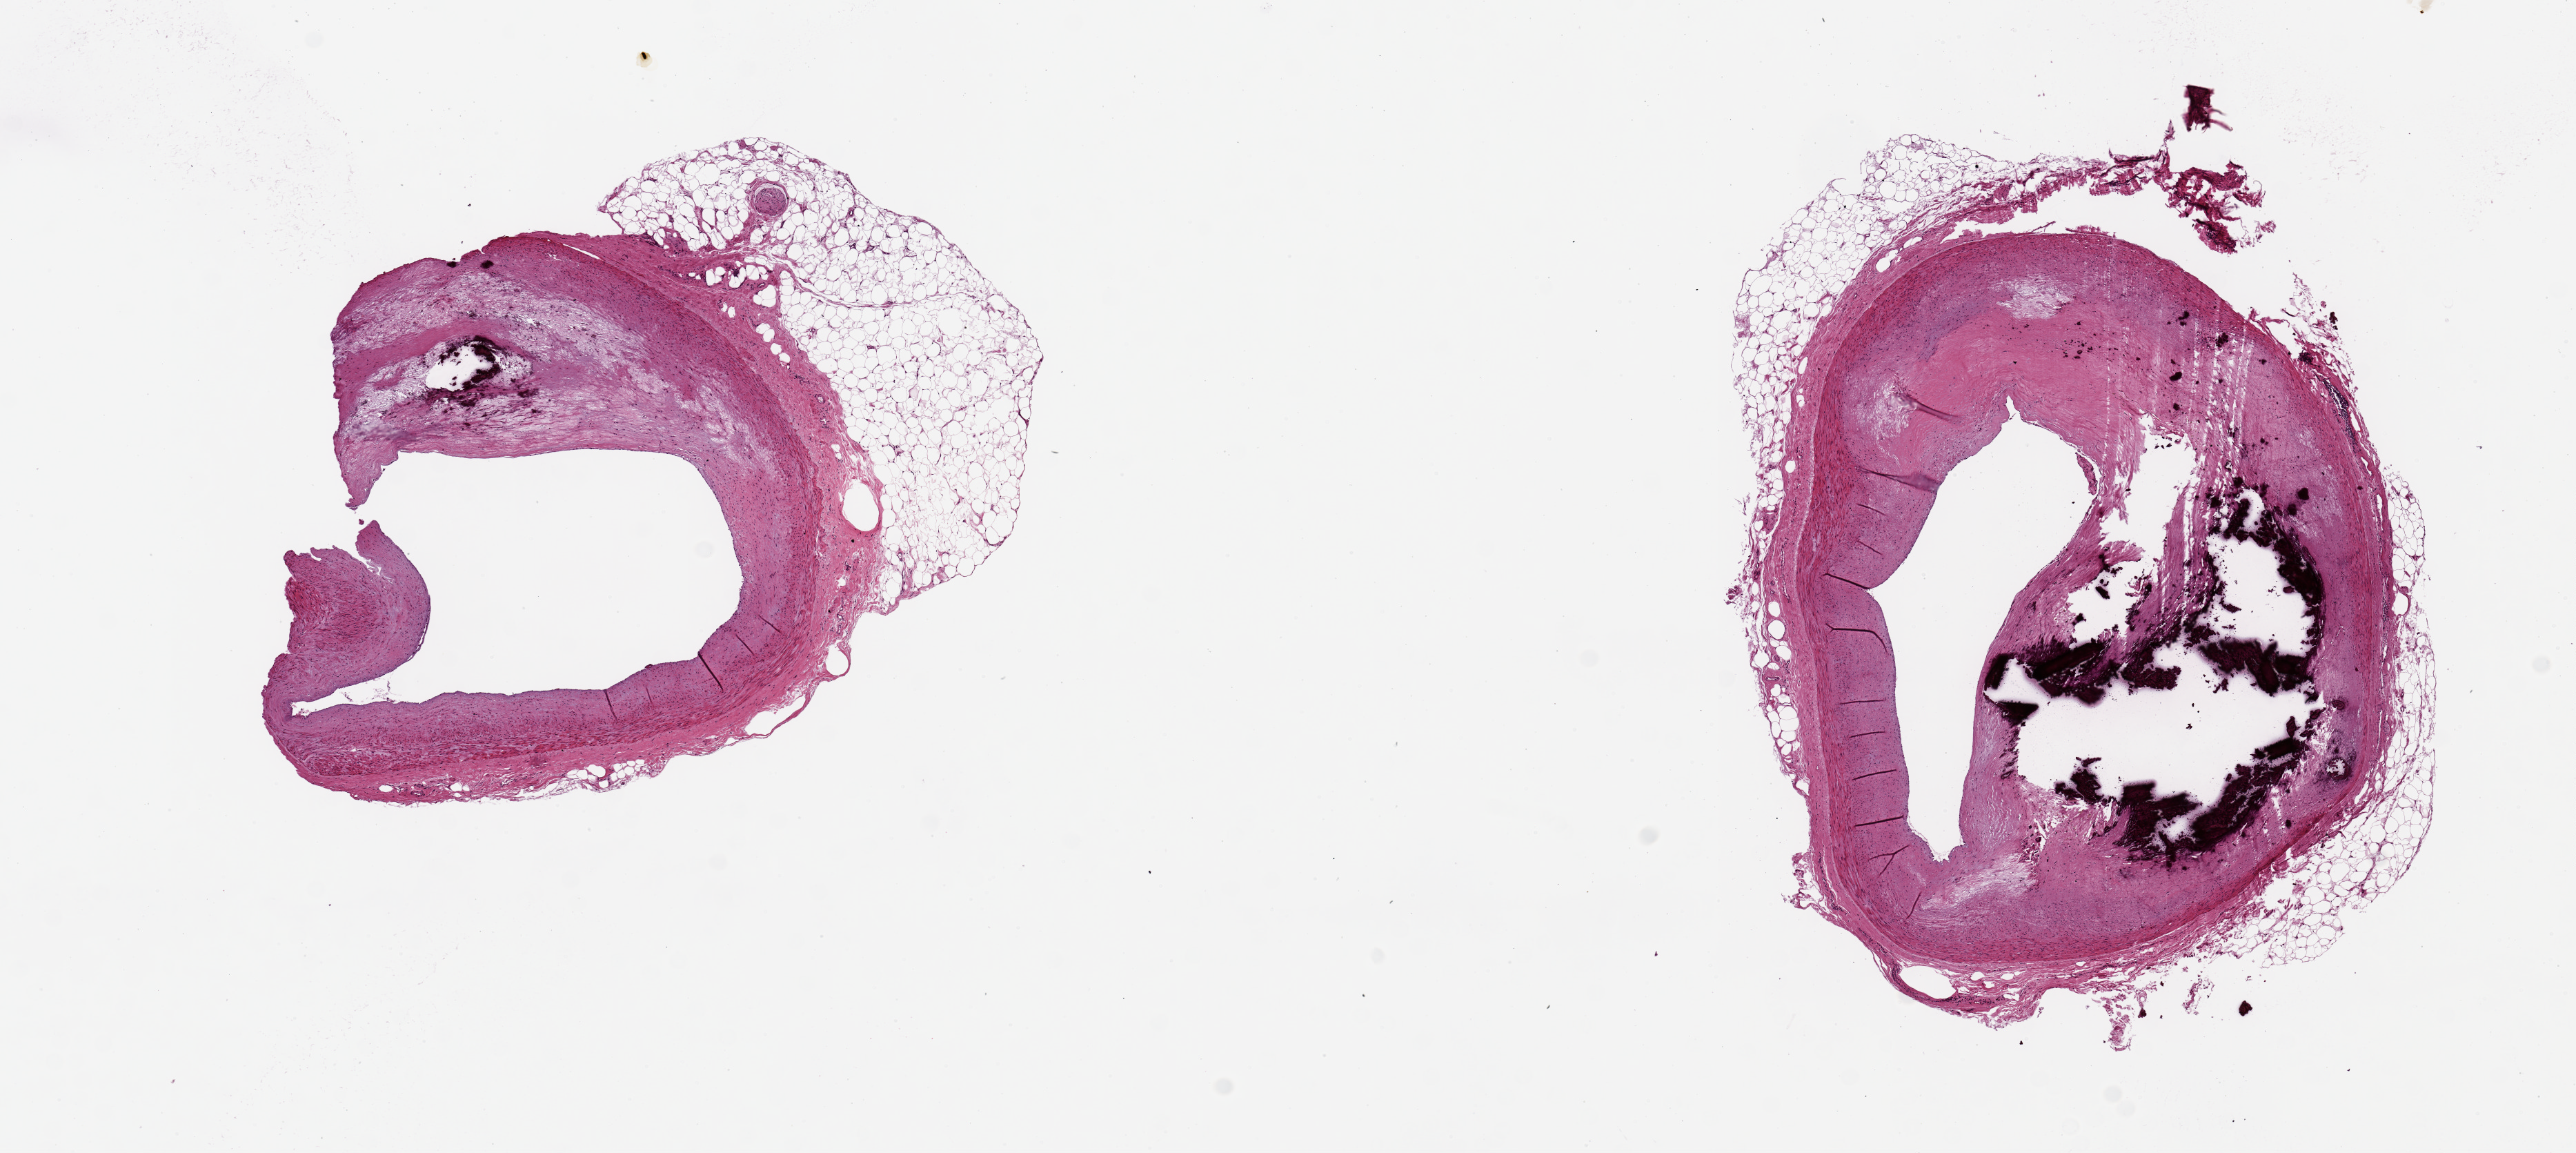
Digitized haematoxylin and eosin-stained section — a low-resolution overview of the entire scanned area, about 14.8 x 6.6 mm; PAXgene-fixed paraffin-embedded (PFPE) section; sampled site (target tissue): coronary artery; tissue donor sample. Male donor.
- review note (as recorded): 2 pieces ~3mm d; 60% occlusive calcifying atherosclerosis